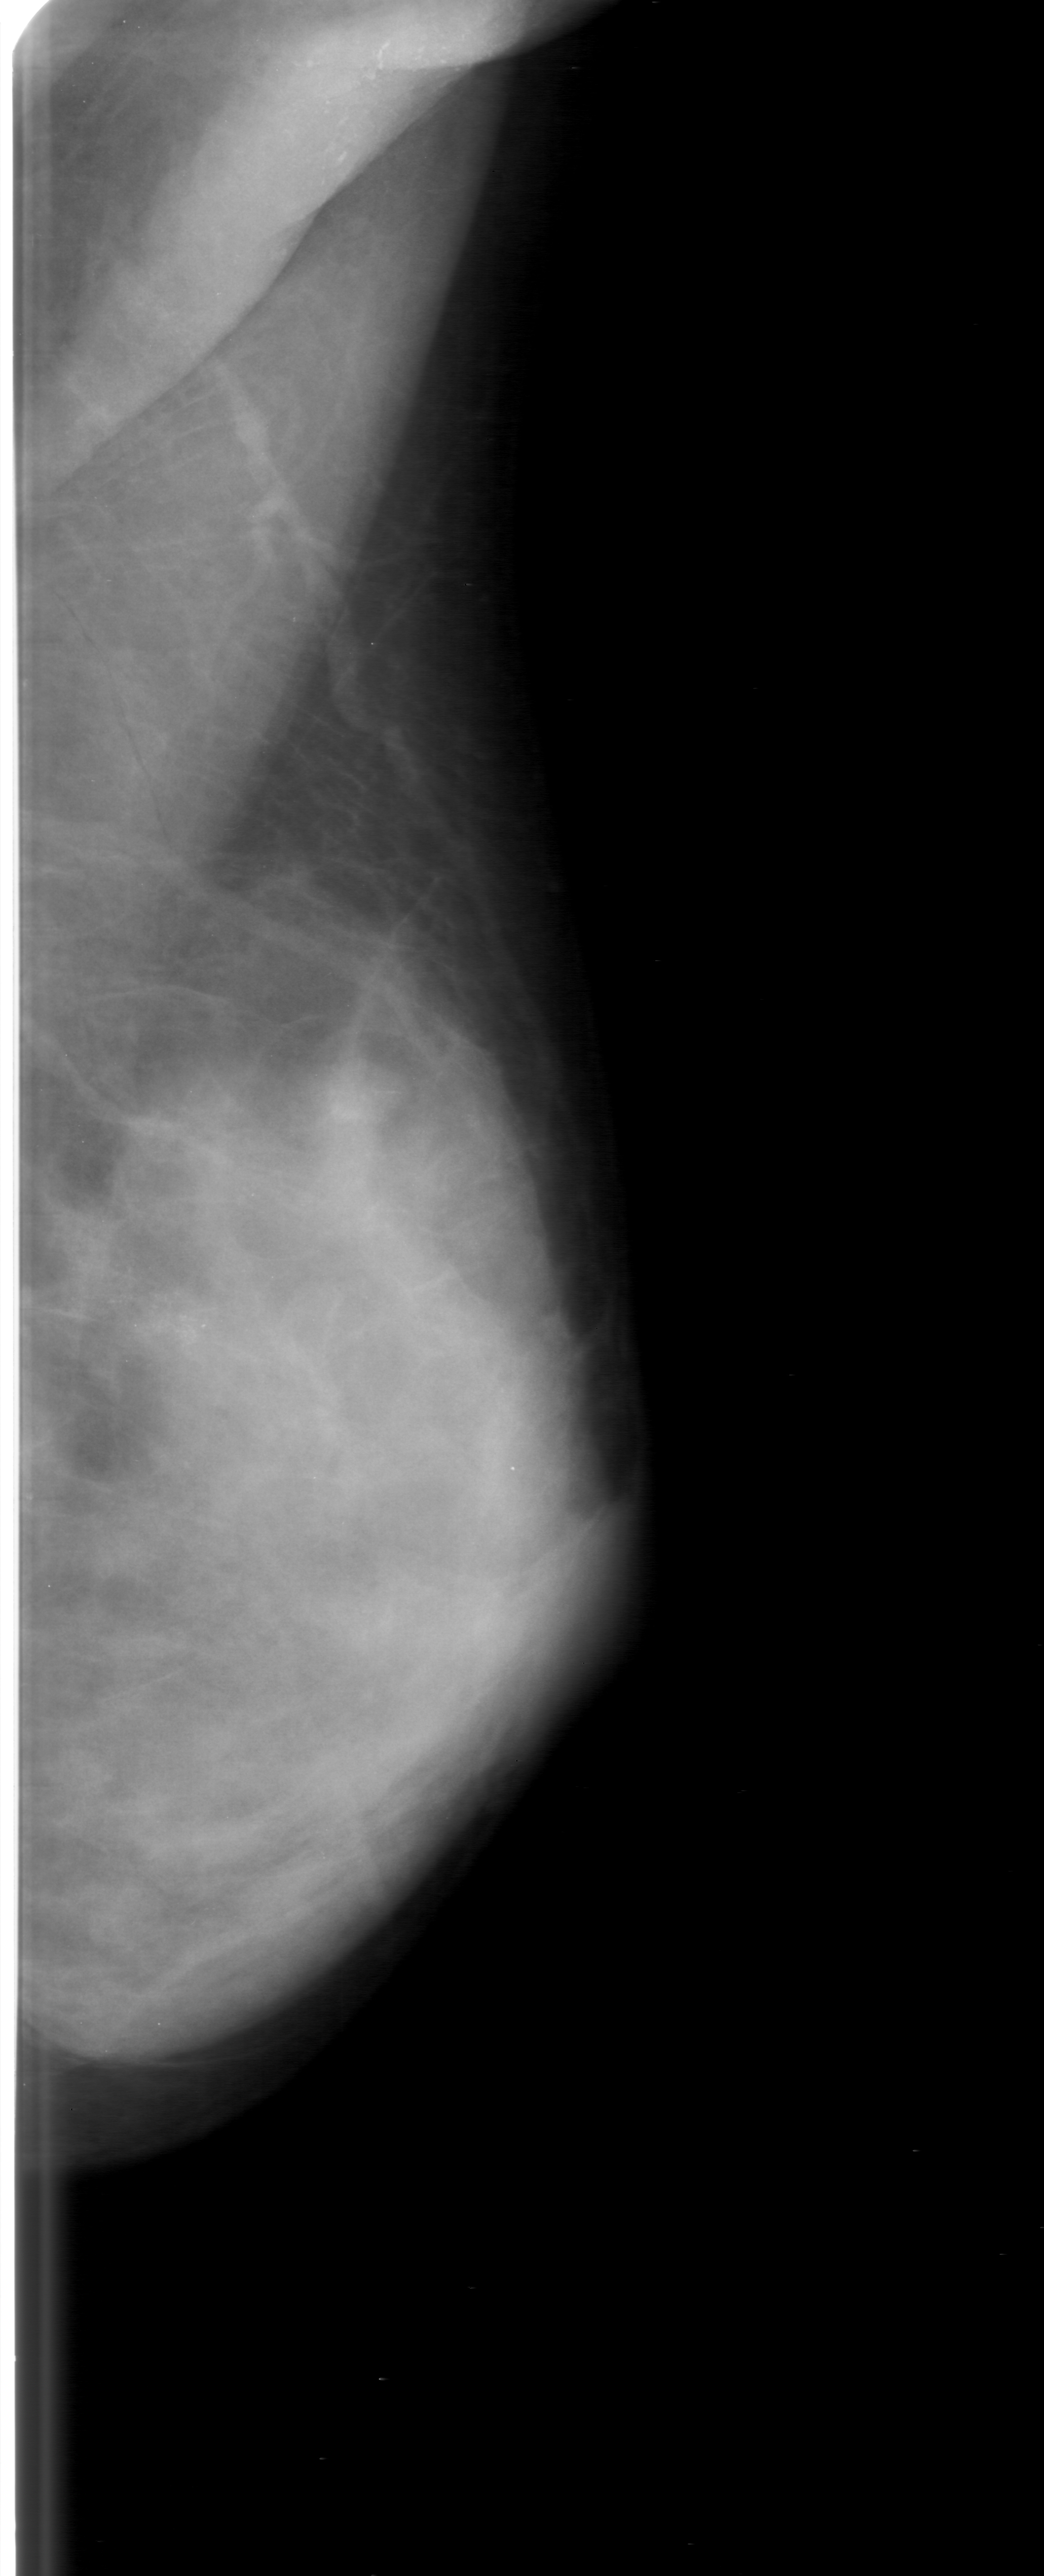
Mammogram (digitized film). Left breast. MLO view. BI-RADS breast density category 3 (scale 1–4). 1044 × 2576 image matrix.
Expert-marked regions of interest on this film, with their recorded descriptors:
- calcifications, morphology fine linear branching, distribution linear; BI-RADS assessment category 3; pathology result (as recorded, not read from the image): malignant: box from (x=16, y=1140) to (x=341, y=1508) px